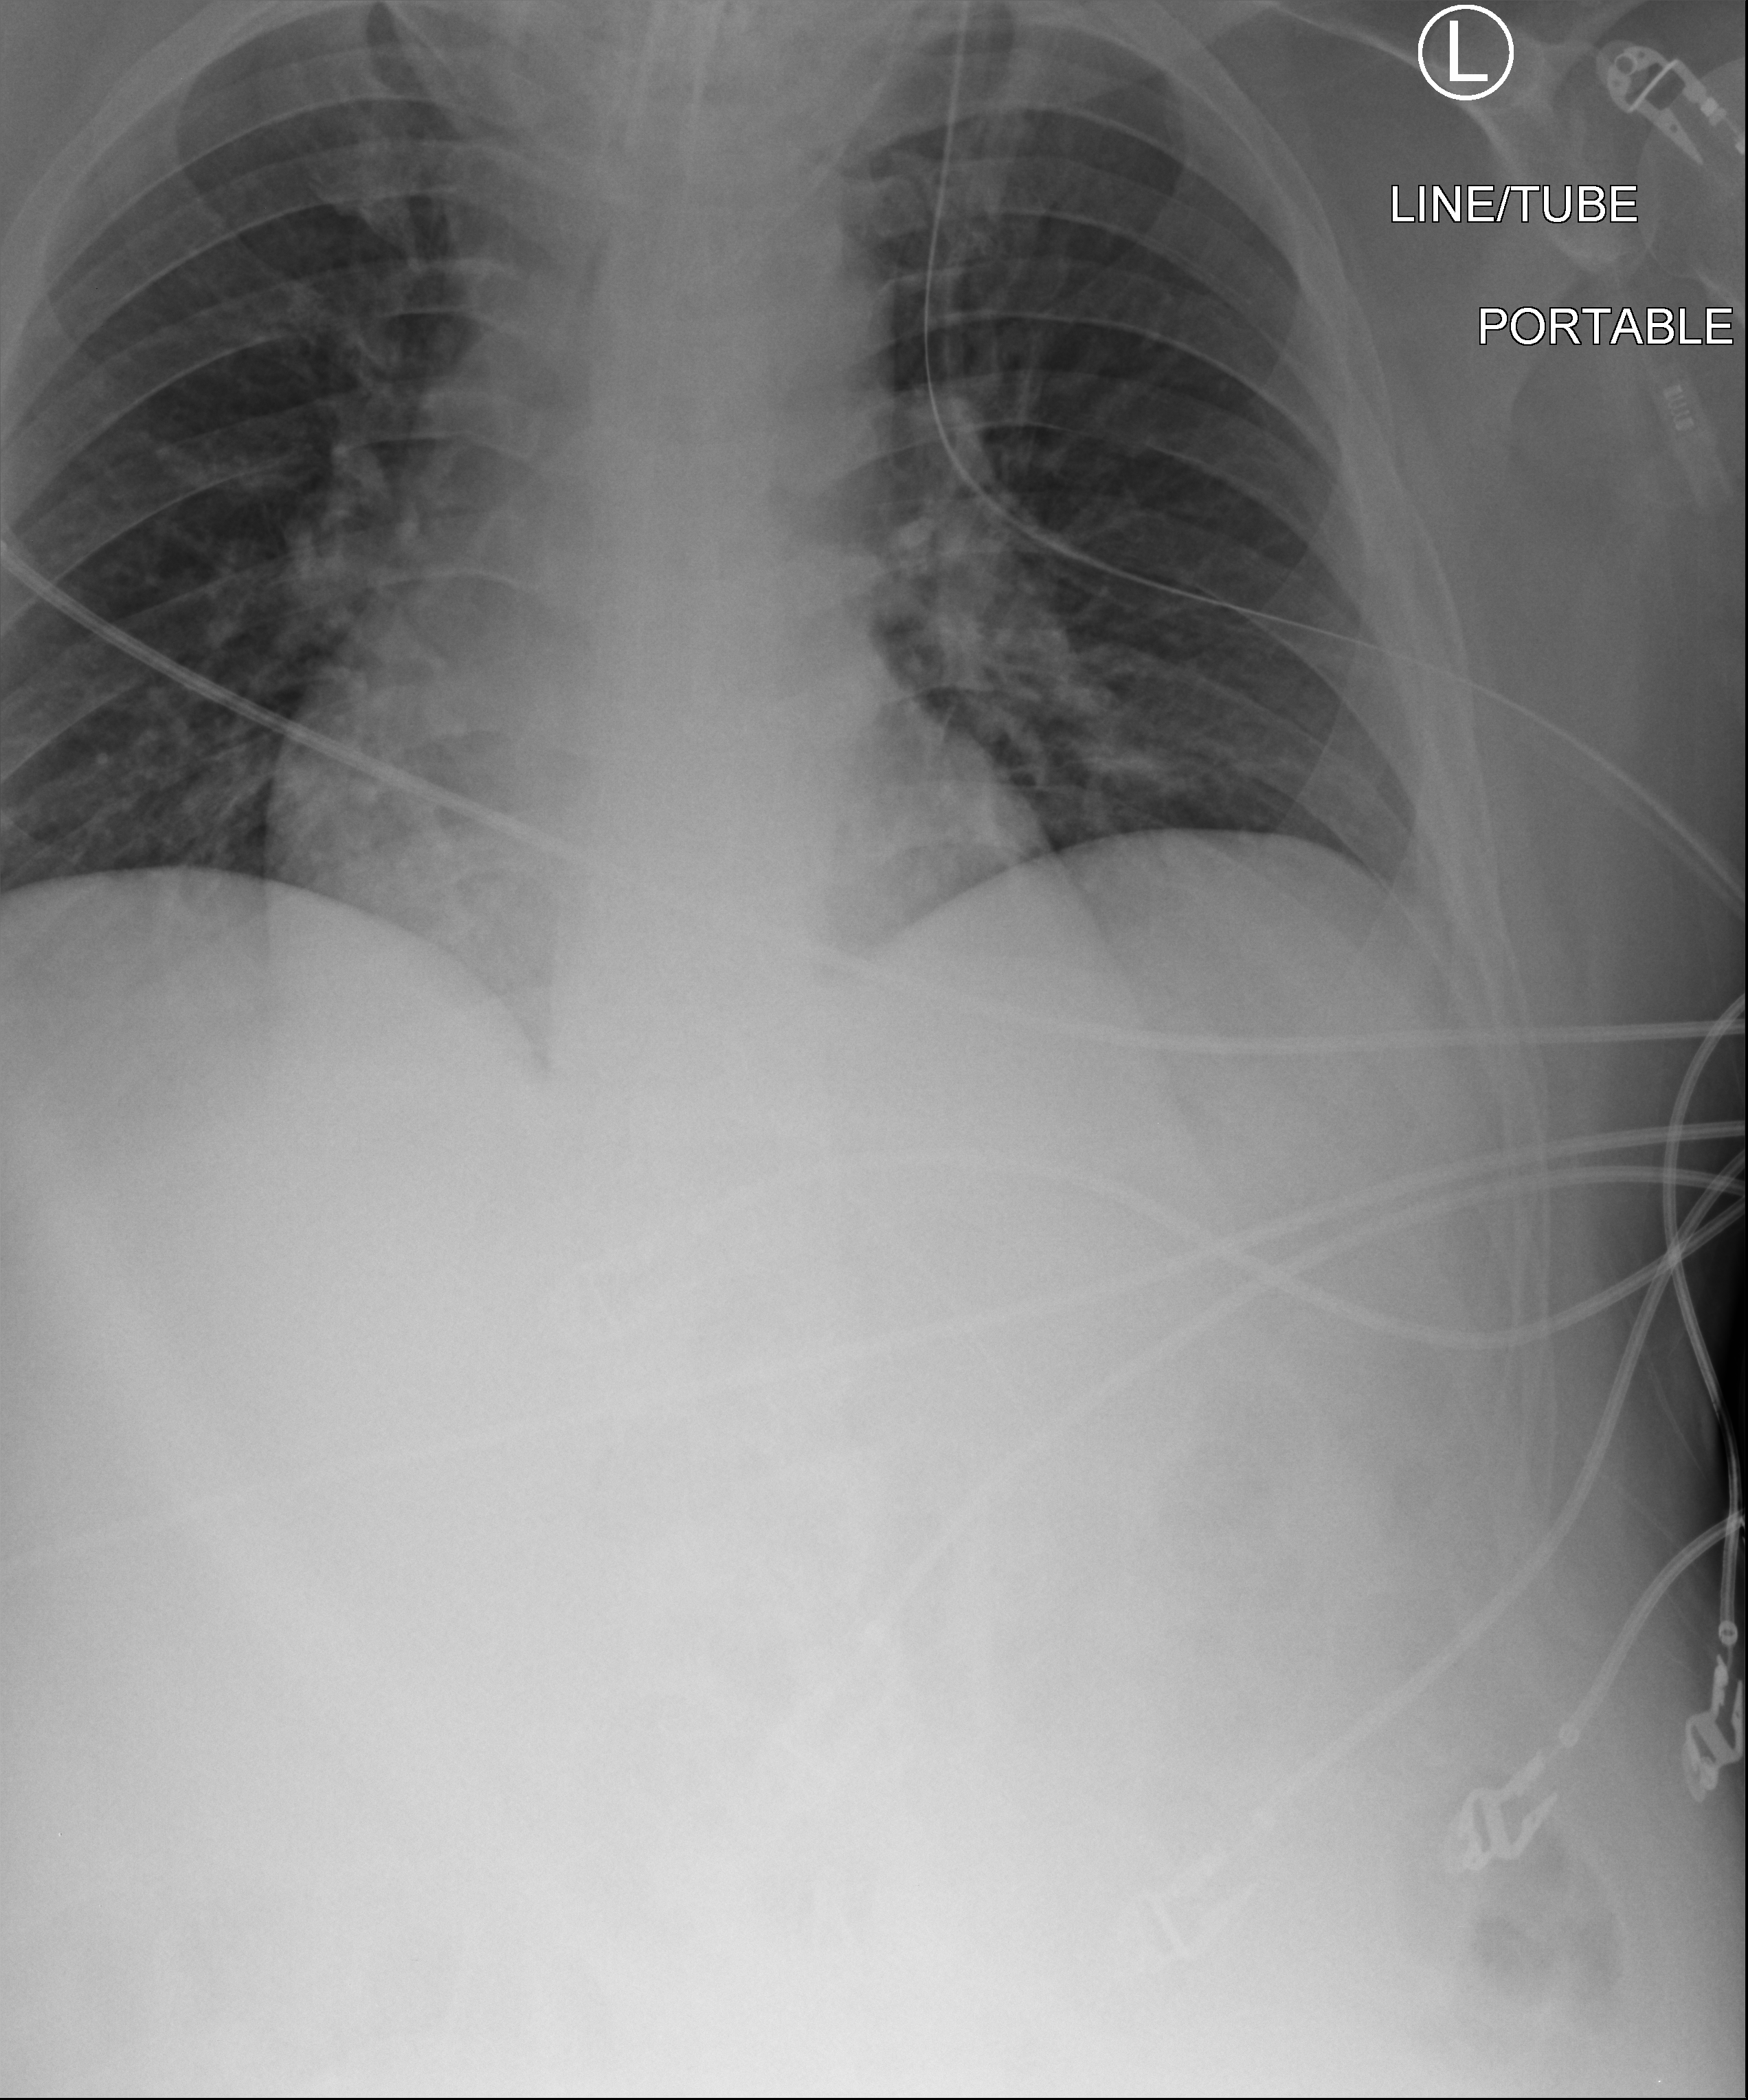
Portable chest radiograph, anteroposterior (AP) projection. Patient hospitalised with COVID-19; male, aged 18–59 years.
From the hospital-stay record, not from the radiograph (when in the stay this image was taken is not recorded):
- mechanically ventilated during this hospital stay: yes